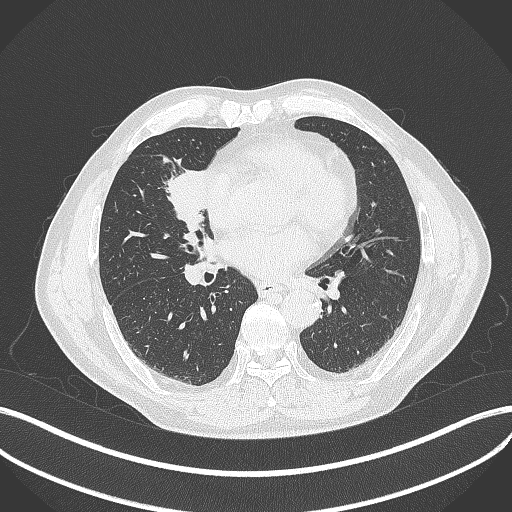
Chest CT, one axial slice; position 187 of 429 along the scan axis; lung window (W 1500 / L -600 HU); 1 mm slice thickness; 512 × 512 image matrix. Patient: male, 61 years. Case-level facts recorded for this patient, not image findings: clinical TNM (as recorded): T2b N1 M0.
Annotated regions visible in this slice (rectangle marked by the reading radiologist):
- lung tumour (recorded histology: squamous cell carcinoma): bounding box [x1, y1, x2, y2] px = [158, 159, 213, 229]